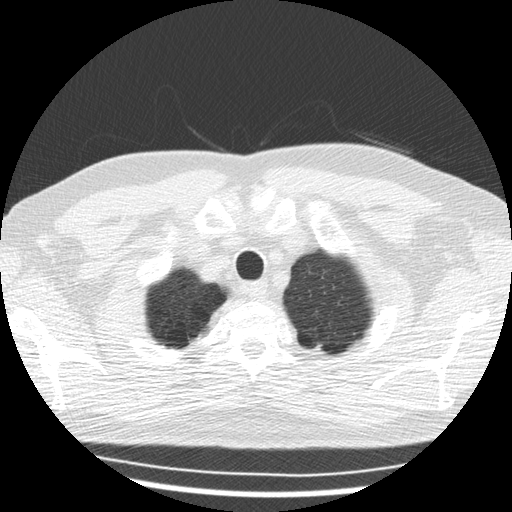
Low-dose screening chest CT, axial slice; first (baseline) screen; lung window (W 1500 / L -600 HU); 2.5 mm slice thickness; 512 × 512 image matrix, field of view 351 × 351 mm. Male participant, aged 57 years at enrolment. Former smoker at enrolment.
Expert-annotated lung lesion, bounding box <305,332,333,356> (left, top, right, bottom; pixels). The exam's reader record, not a measurement of the box and not confirmed to be the same lesion: non-calcified nodule or mass ≥4 mm, right upper lobe, 7 × 6 mm, smooth margins, soft tissue attenuation. Note: the box lies in the patient's left hemithorax on this image, whereas the reader's record names the right lung; they may be different findings. Participant outcome: lung cancer diagnosed 674 days after this screen (after the second annual screen) — adenocarcinoma, NOS, left upper lobe, stage IV (AJCC 6th edition), 50 mm at pathology.